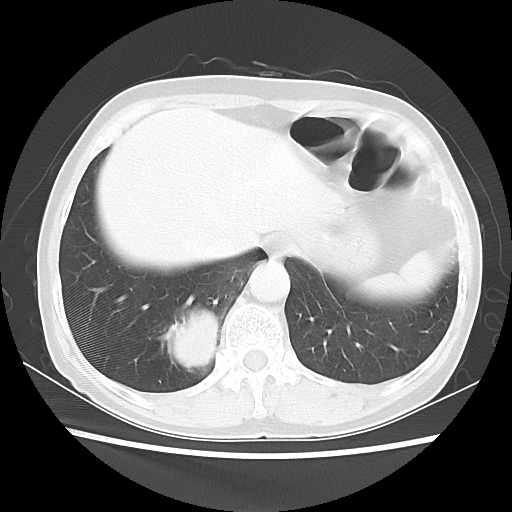
Chest CT, one axial slice. Slice 10 of 56 in the series (ordered by position). Reconstruction kernel LUNG. 120 kVp. Lung window (W 1500 / L -600 HU). 5 mm slice thickness. 512 × 512 image matrix, field of view 332 × 332 mm. Female patient, age 66 years. From the clinical record (not read from this slice): clinical TNM (as recorded): T2 N3 M0; histopathological grade: G3.
Annotated regions visible in this slice (bounding box drawn by a radiologist):
- lung tumour (recorded histology: small cell carcinoma): bounding box <163,298,228,386> (left, top, right, bottom; pixels)